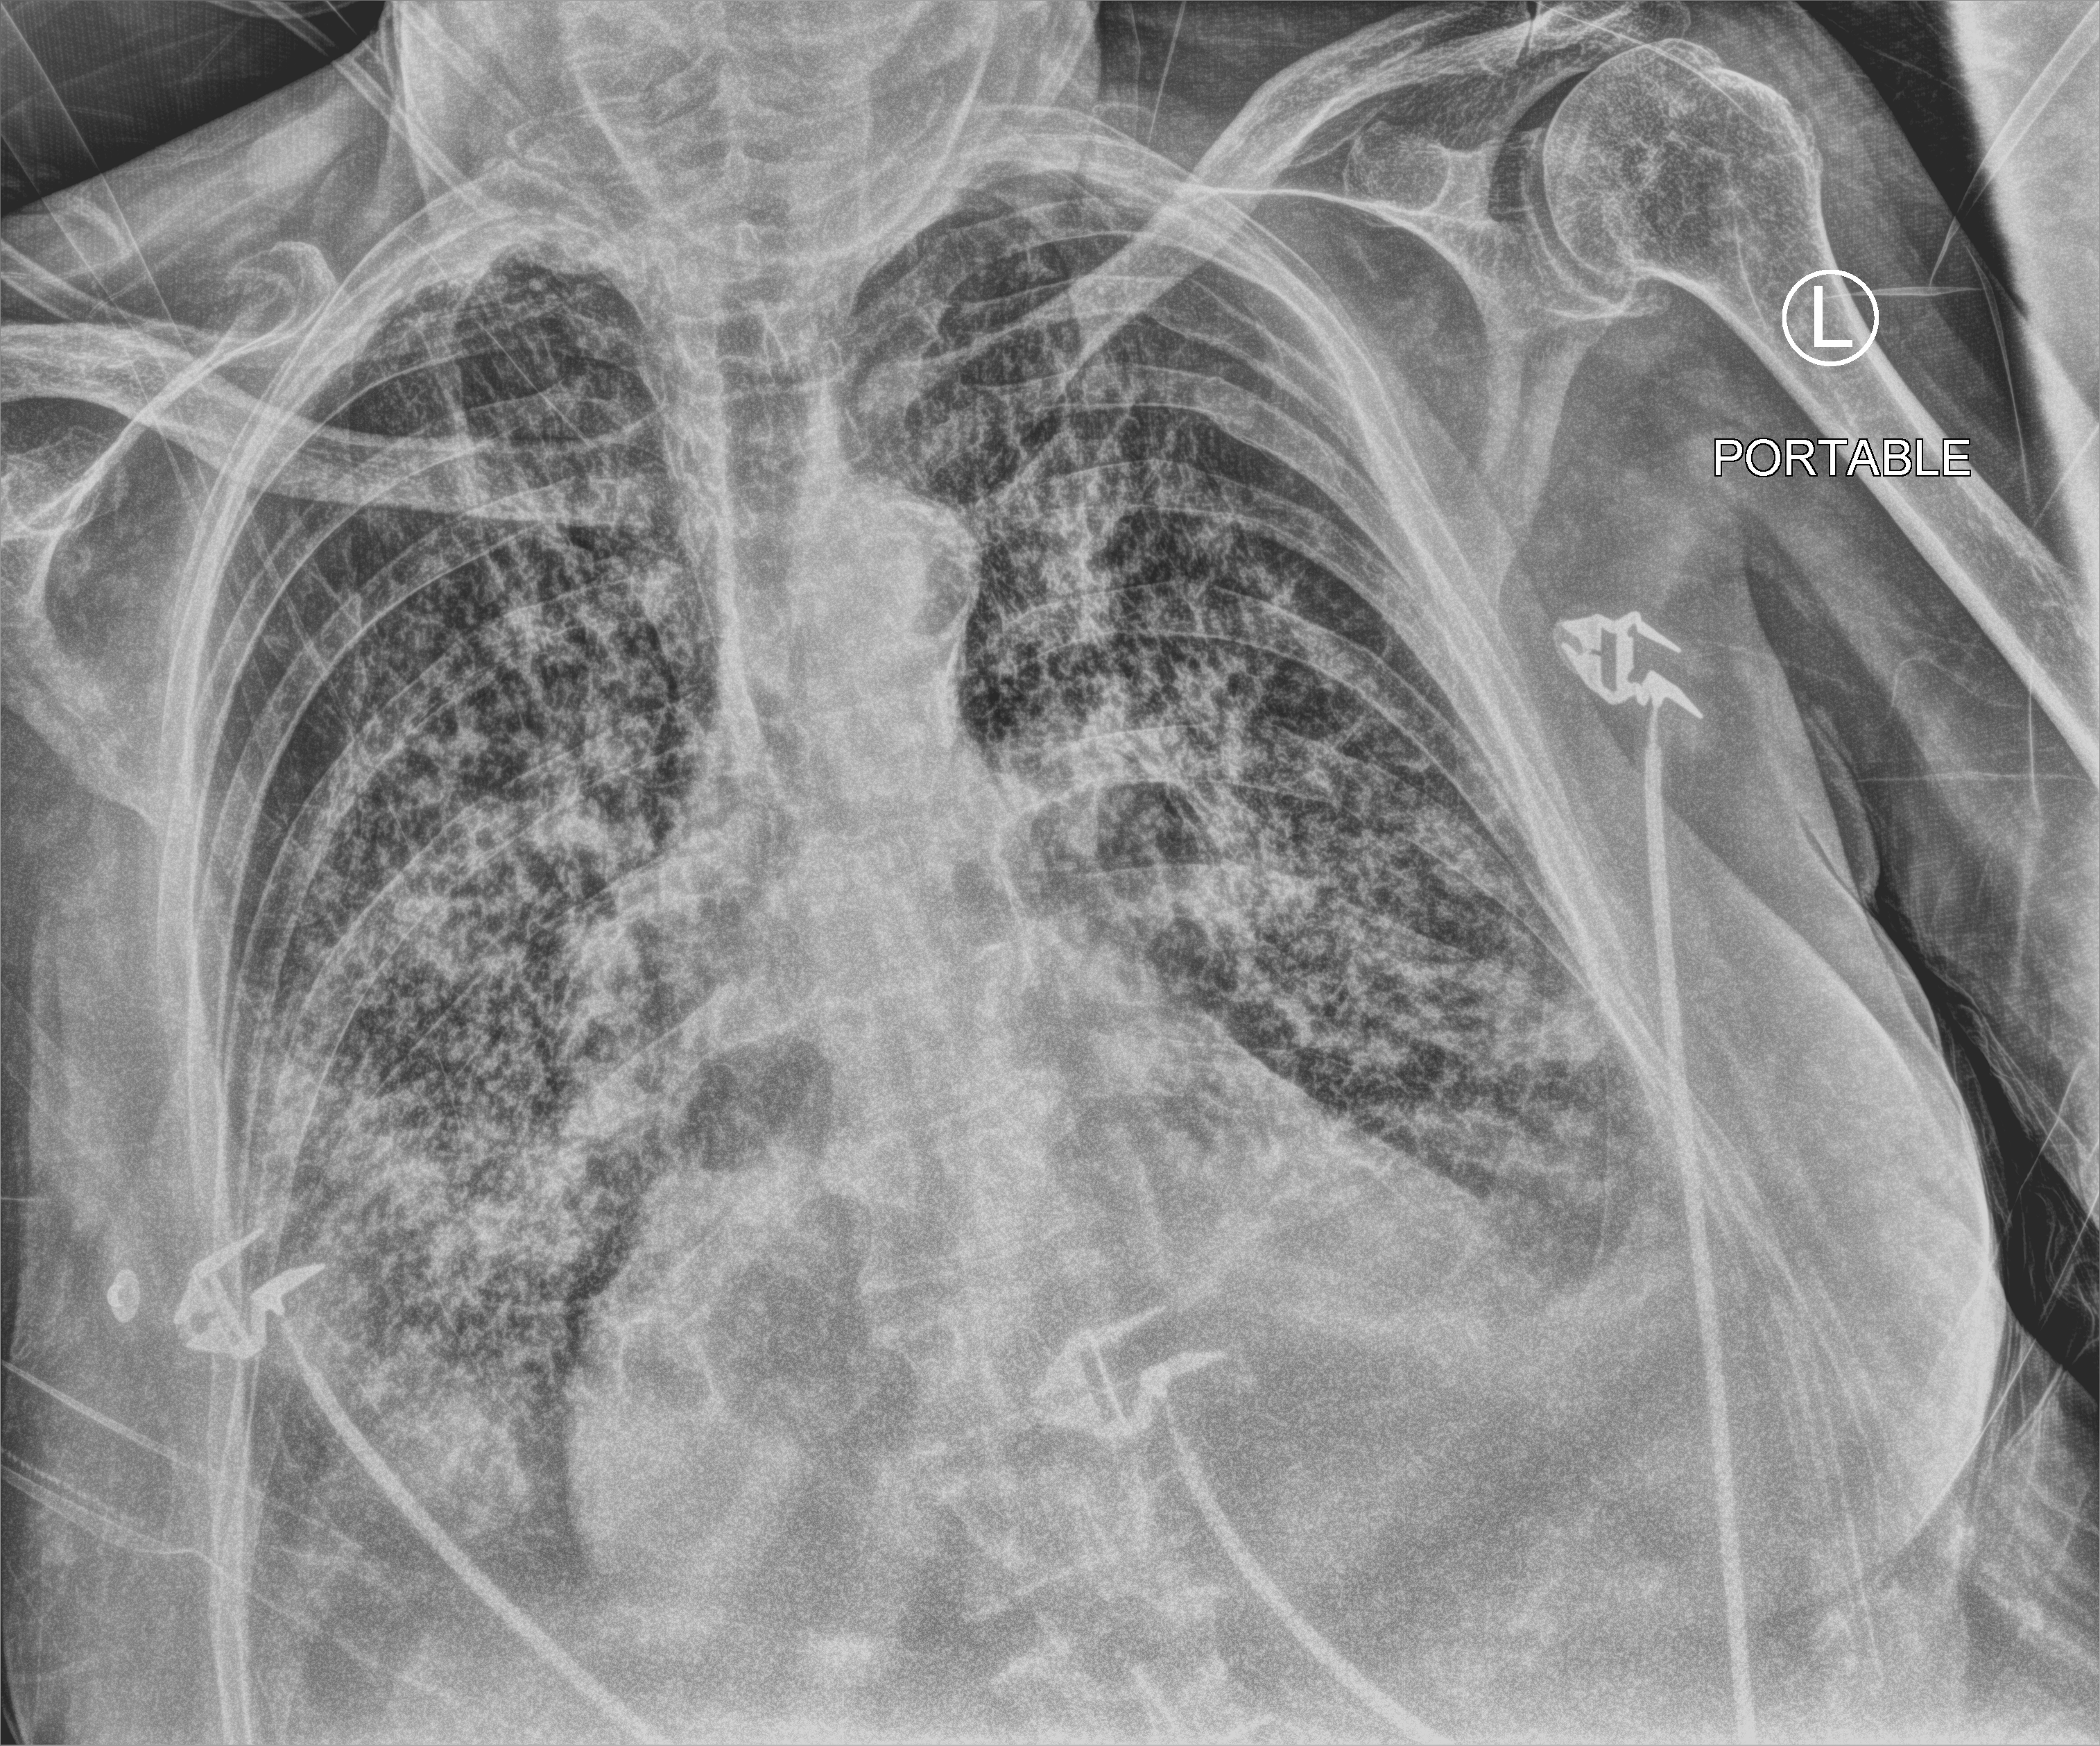
Bedside chest radiograph (computed radiography), anteroposterior (AP) projection. Male patient hospitalised with COVID-19, age 75–90 years.
From the hospital-stay record, not from the radiograph (when in the stay this image was taken is not recorded): mechanically ventilated during this hospital stay: no.